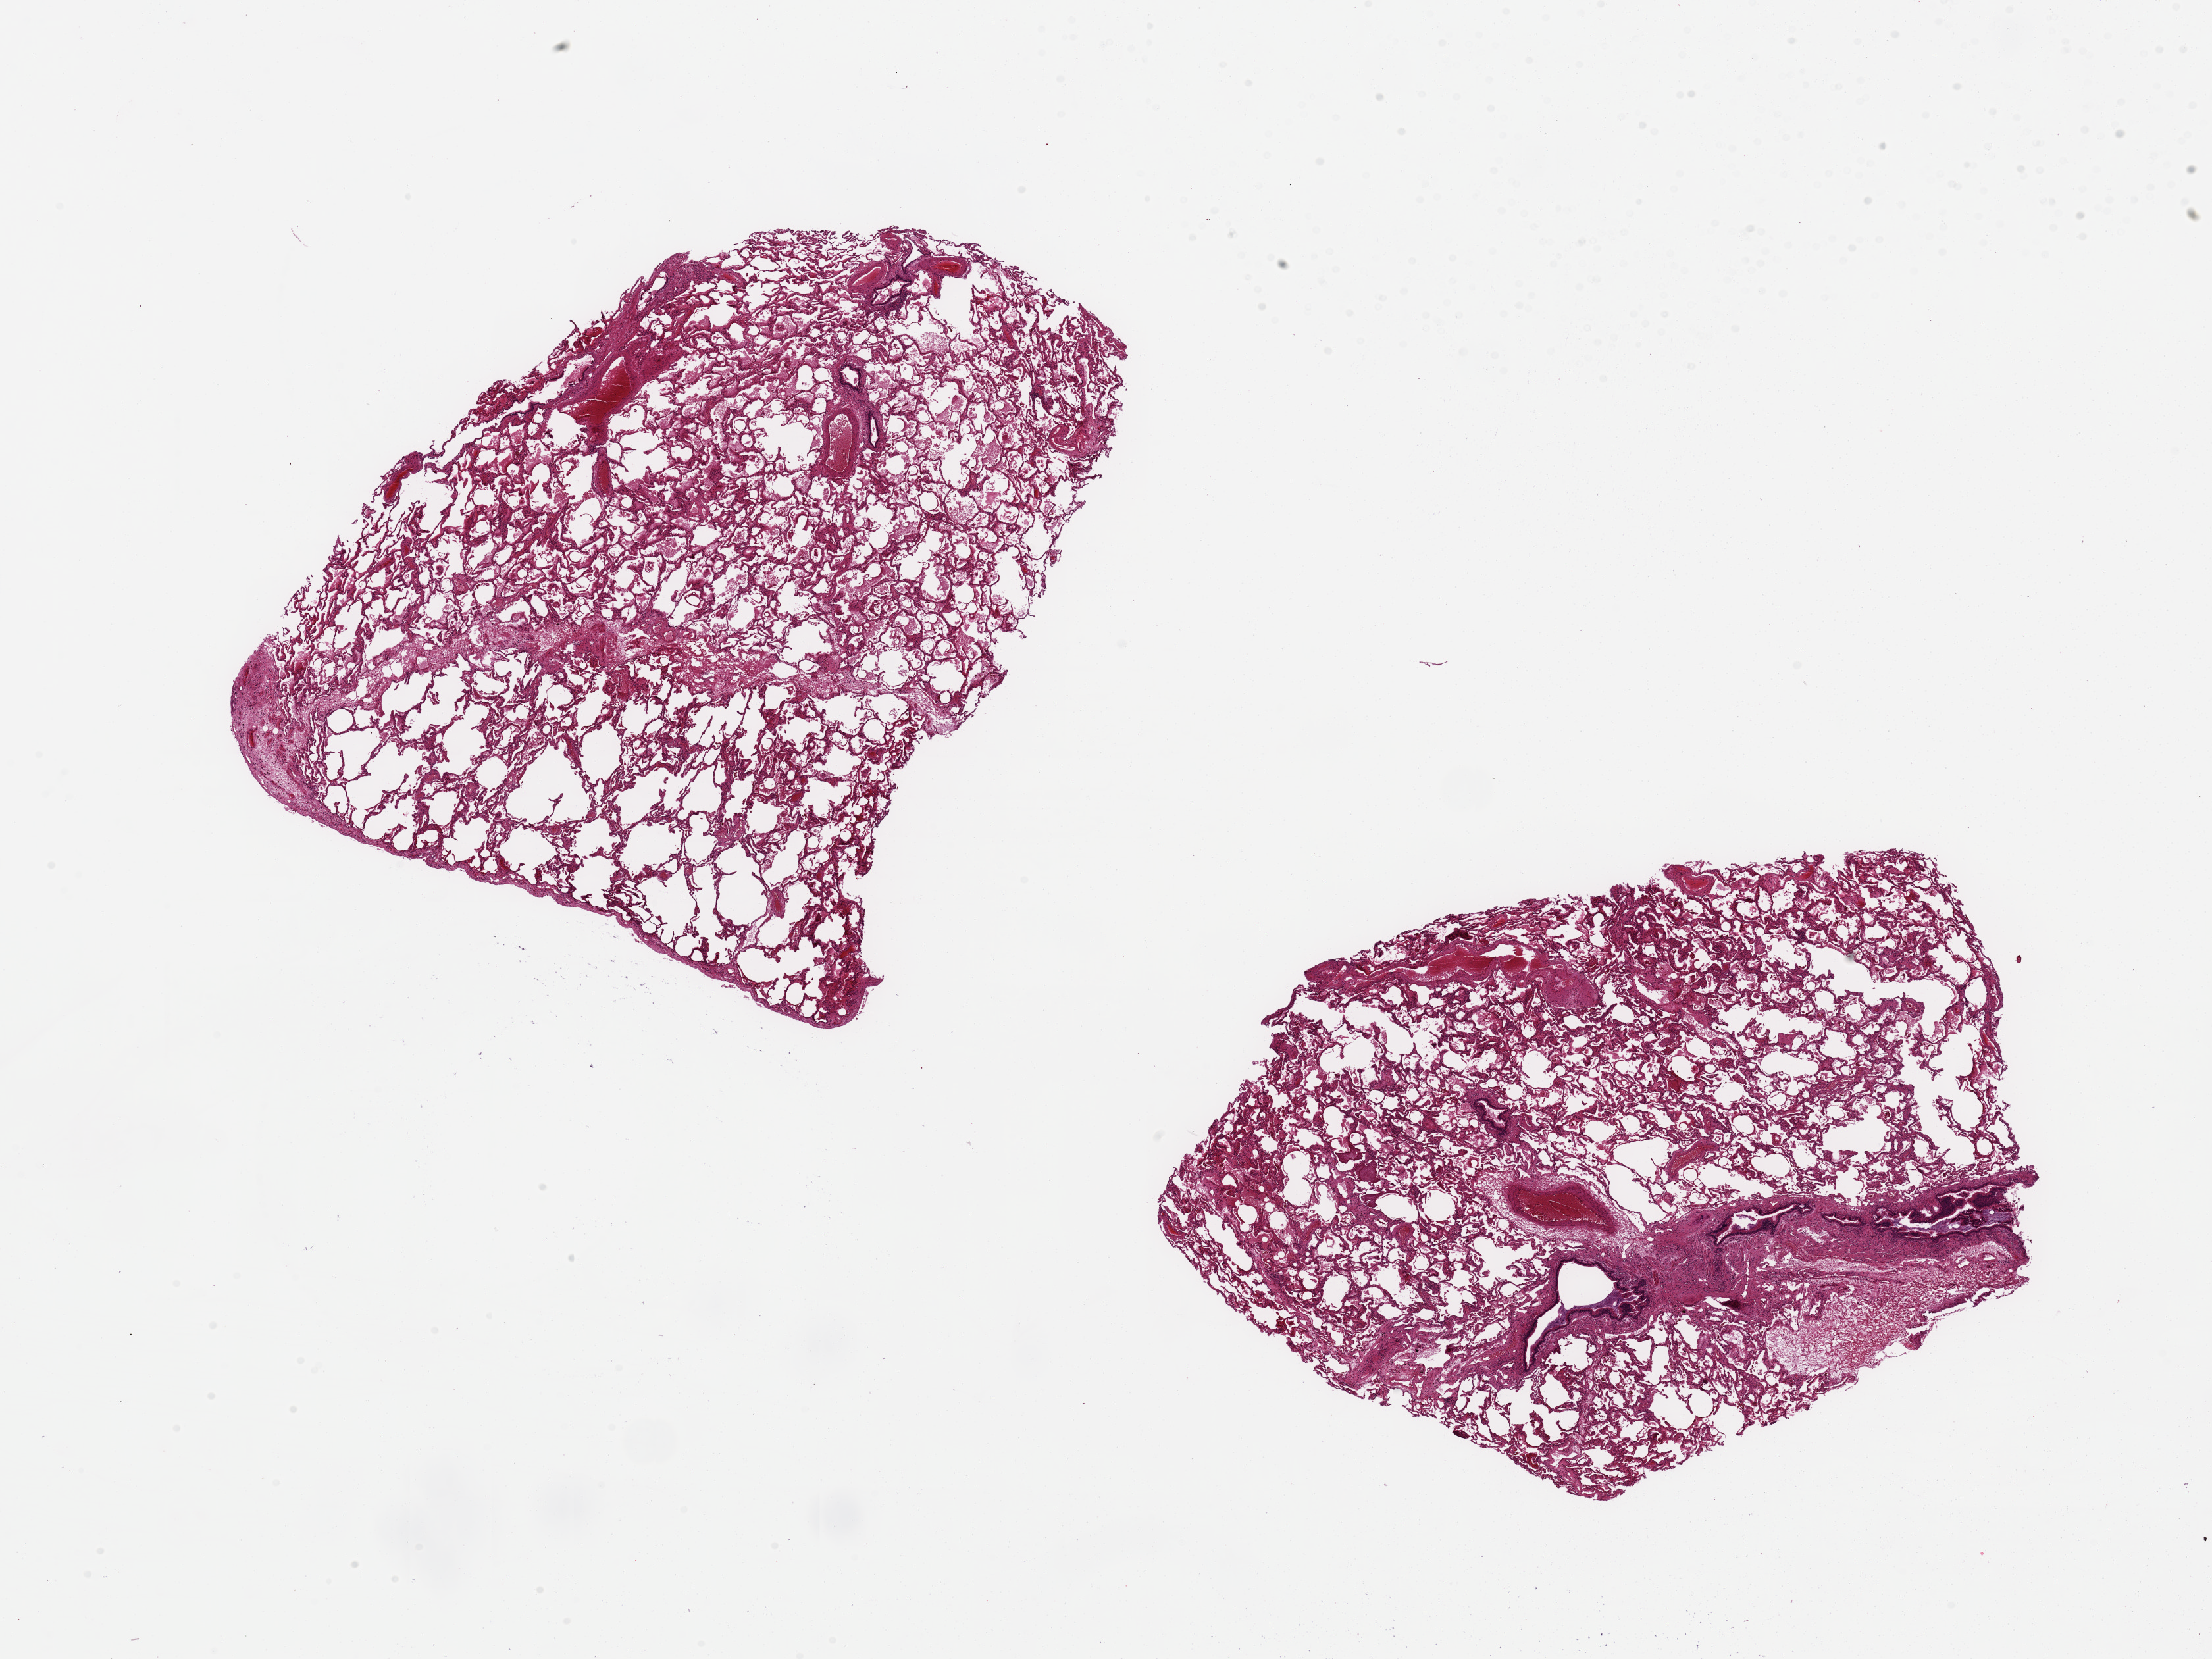
Whole-slide image, haematoxylin and eosin stain — a low-resolution overview of the entire scanned area, about 26.6 x 19.9 mm (from a 20x scan). PAXgene-fixed paraffin-embedded (PFPE) section. Target tissue: lung. Tissue donor sample. Male donor.
- review note (as recorded): 2 ~9x8mm pieces. Mild edema, focal mucus plugging in bronchioles